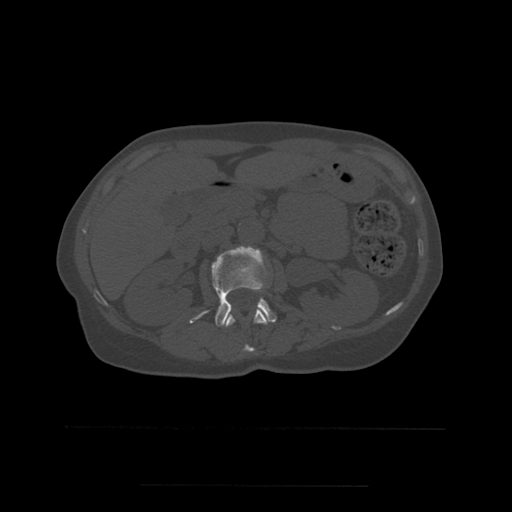
CT including the spine, one axial slice; position 221 of 544 along the scan axis; bone window (W 1800 / L 400 HU); 1.25 mm slice thickness; 512 × 512 image matrix. Patient age 58 years. Case-level facts recorded for this patient, not image findings: primary cancer: lung.
Annotated regions visible in this slice (semi-automatically segmented with operator editing):
- L1 vertebra: bounding box [x1, y1, x2, y2] px = [226, 310, 268, 353]
- L2 vertebra: [190, 246, 277, 327]